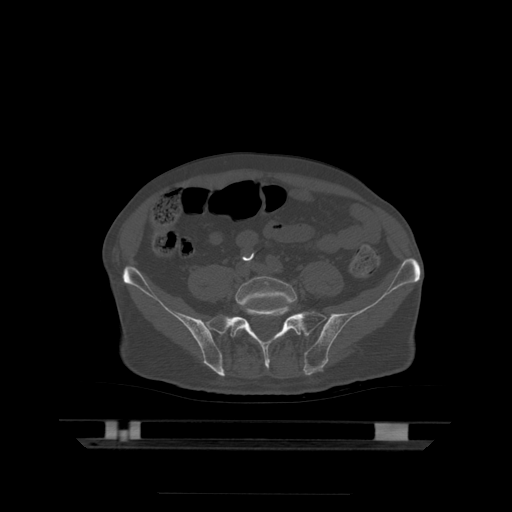
CT including the spine, one axial slice; position 62 of 522 along the scan axis; bone window (W 1800 / L 400 HU); 1.25 mm slice thickness; 512 × 512 image matrix, field of view 436 × 436 mm. Patient age 68 years. Case-level facts recorded for this patient, not image findings: primary cancer: urothelial.
Annotated regions visible in this slice (semi-automatically segmented with operator editing):
- L5 vertebra: box from (x=236, y=276) to (x=298, y=335) px